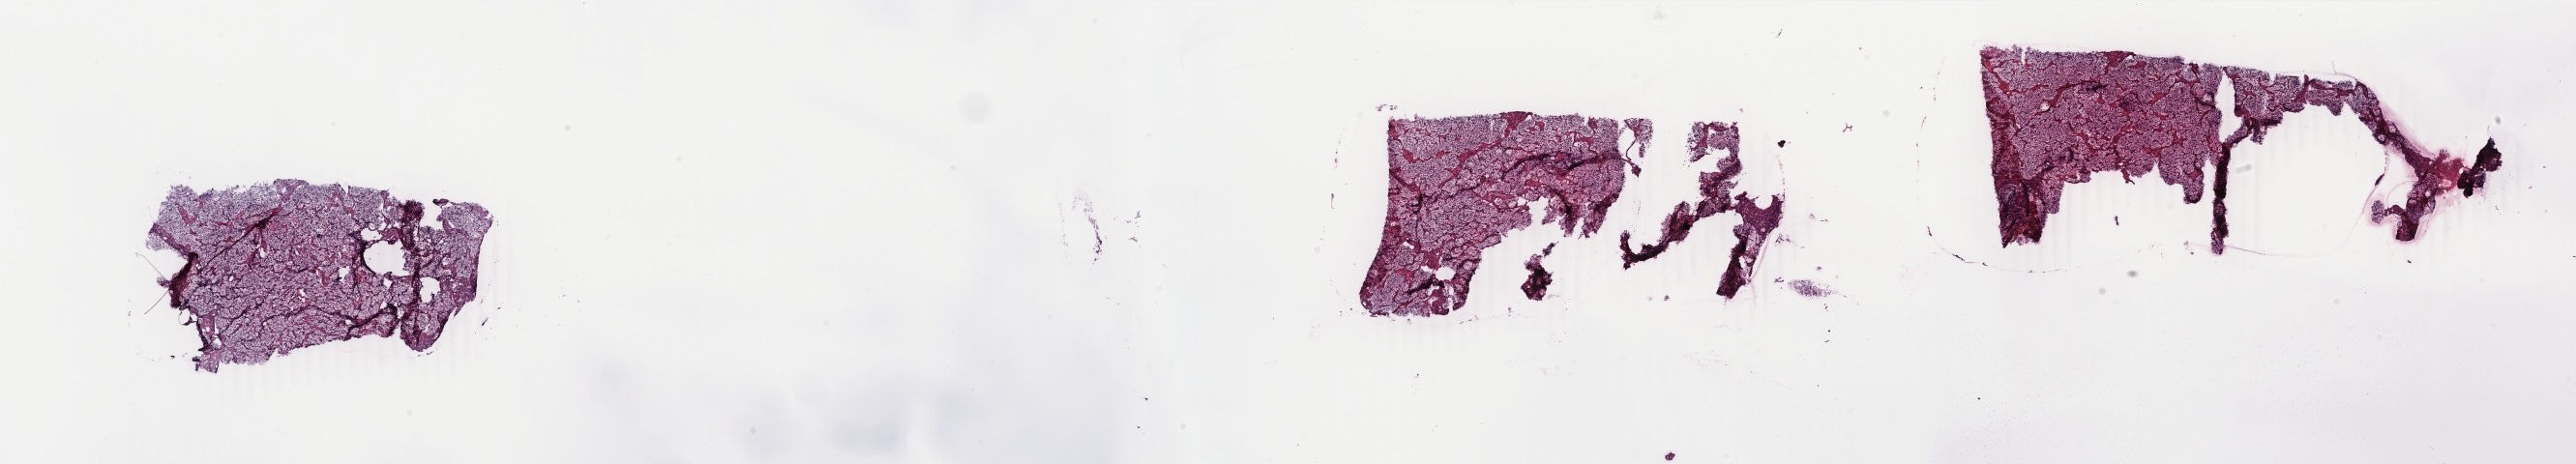
H&E whole-slide image, shown as a low-resolution overview of the whole scanned area (about 42.4 x 7.6 mm, slide scanned at 40x); frozen section; primary tumour sample from the colon. Female patient; age at initial diagnosis 52 years. Slide review estimates, as recorded: tumour cells 95%, tumour nuclei 75%, normal cells 5%, stromal cells 0%, necrosis 0%. Inflammatory infiltration, as recorded: lymphocyte infiltration 0%, monocyte infiltration 0%, neutrophil infiltration 0%.
AJCC pathologic stage: IIA (6th edition). Lymph nodes positive (case pathology): 0 of 13 examined. Pathologic diagnosis: Mucinous adenocarcinoma (cecum). TNM: T3 N0 MX.